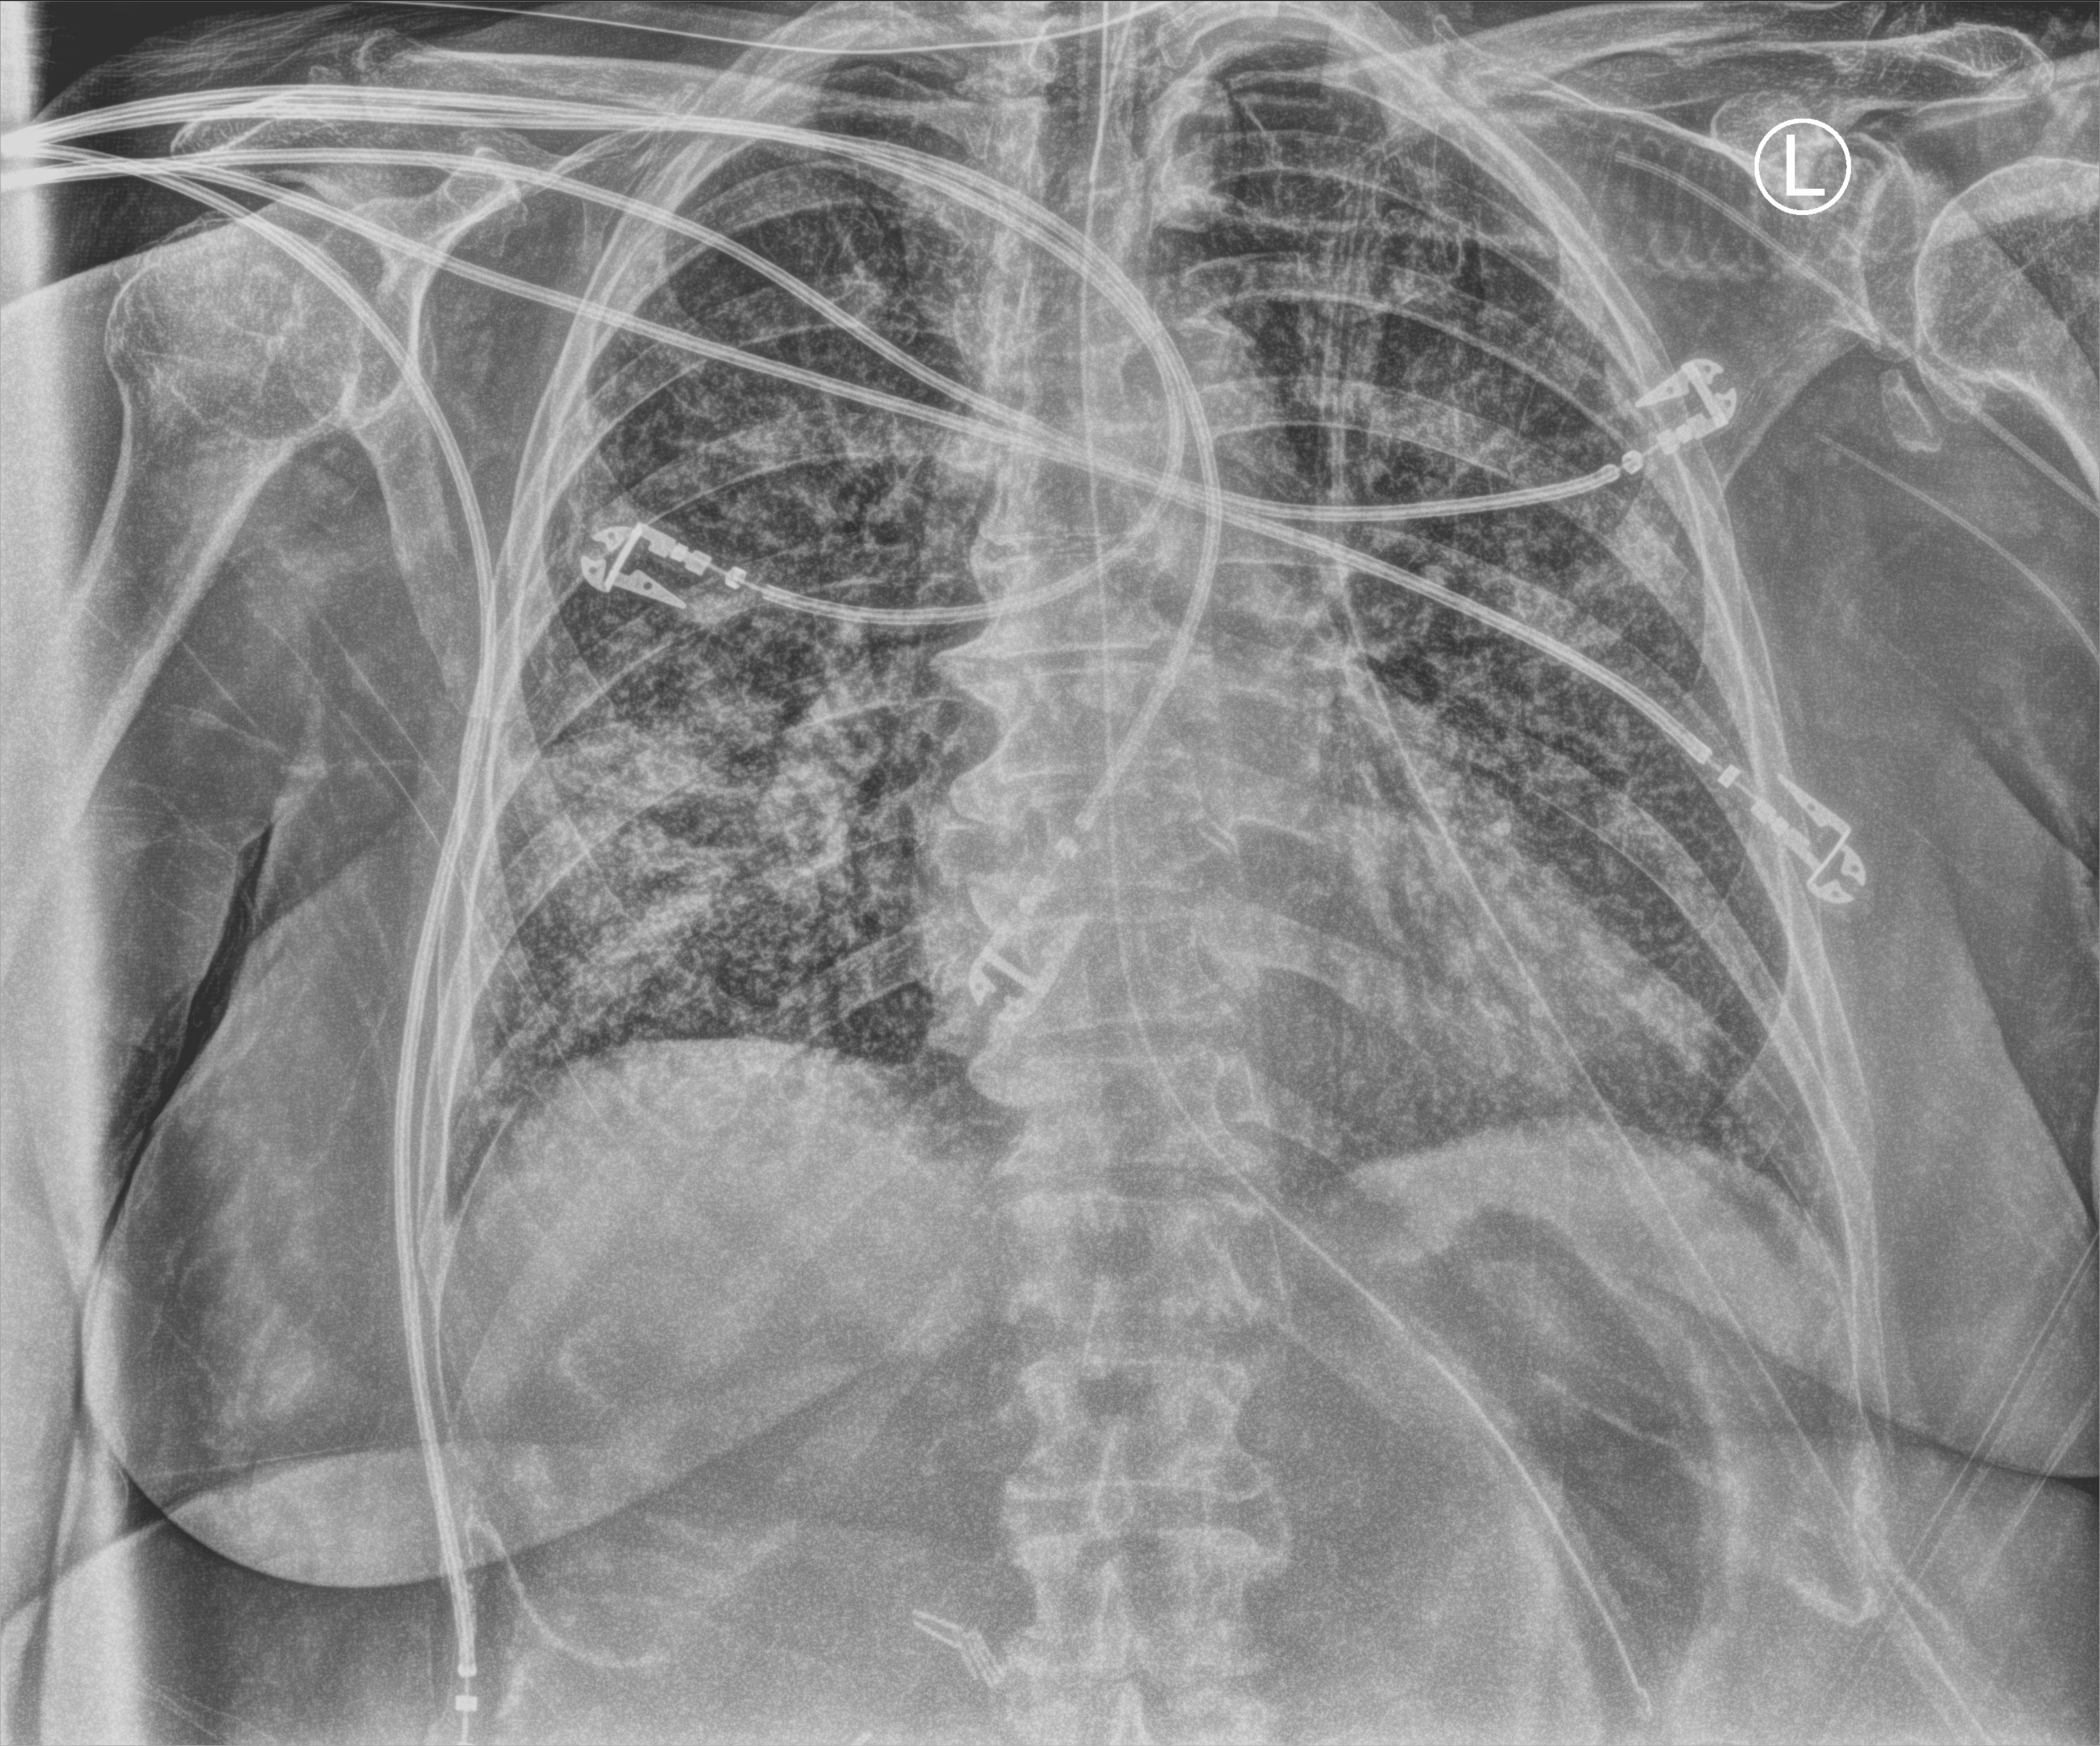
Bedside chest radiograph (computed radiography); anteroposterior (AP) projection. Patient hospitalised with COVID-19; female, aged 75–90 years.
From the hospital-stay record, not from the radiograph (when in the stay this image was taken is not recorded): admitted to intensive care during this hospital stay: no; mechanically ventilated during this hospital stay: yes; length of hospital stay: 56 days.